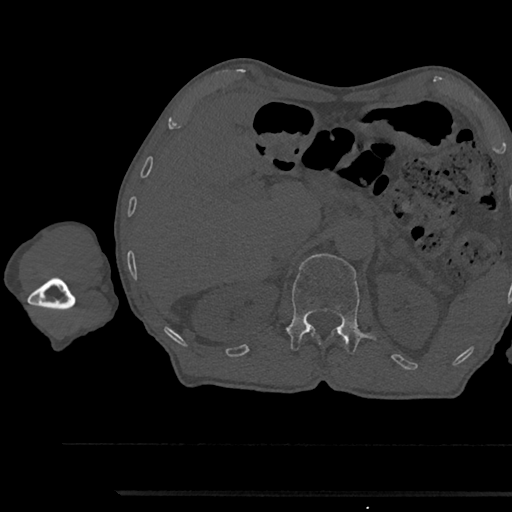
CT including the spine, one axial slice; slice 663 of 797 in the series (ordered by position); reconstruction kernel Br40s/3; 120 kVp; bone window (W 1800 / L 400 HU); 0.5 mm slice thickness; 512 × 512 image matrix, field of view 367 × 367 mm. Male patient, age 79 years. Case-level facts recorded for this patient, not image findings: primary cancer: prostate.
Outlined on this slice (semi-automatically segmented with operator editing):
- L1 vertebra: bounding box (x1, y1, x2, y2) in pixels: (286, 253, 376, 353)